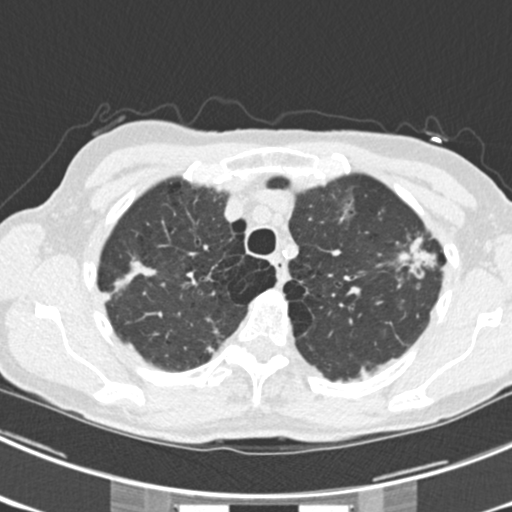
Low-dose screening chest CT, one axial slice; slice 177 of 225 in the series (ordered by position); lung window (W 1500 / L -600 HU); 2 mm slice thickness; 512 × 512 image matrix.
Annotated regions visible in this slice (expert manual segmentation):
- lesion 1 (tumor, upper lobe of left lung): bounding box (x1, y1, x2, y2) in pixels: (397, 236, 436, 279)
- lesion 5 (tumor, upper lobe of right lung): (112, 258, 156, 293)